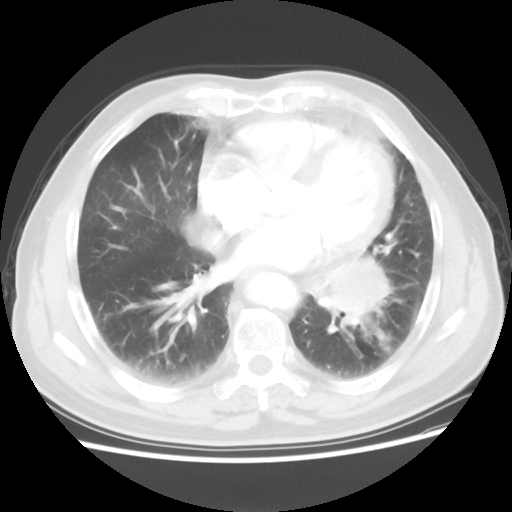
Chest CT, one axial slice. Position 25 of 56 along the scan axis. Reconstruction kernel STANDARD. Lung window (W 1500 / L -600 HU). 5 mm slice thickness. 512 × 512 image matrix, field of view 360 × 360 mm. Patient: male, 75 years. From the clinical record (not read from this slice): clinical TNM (as recorded): T3 N0 M0.
Annotated regions visible in this slice (bounding box drawn by a radiologist):
- lung tumour (recorded histology: squamous cell carcinoma): bounding box <321,255,400,332> (left, top, right, bottom; pixels)